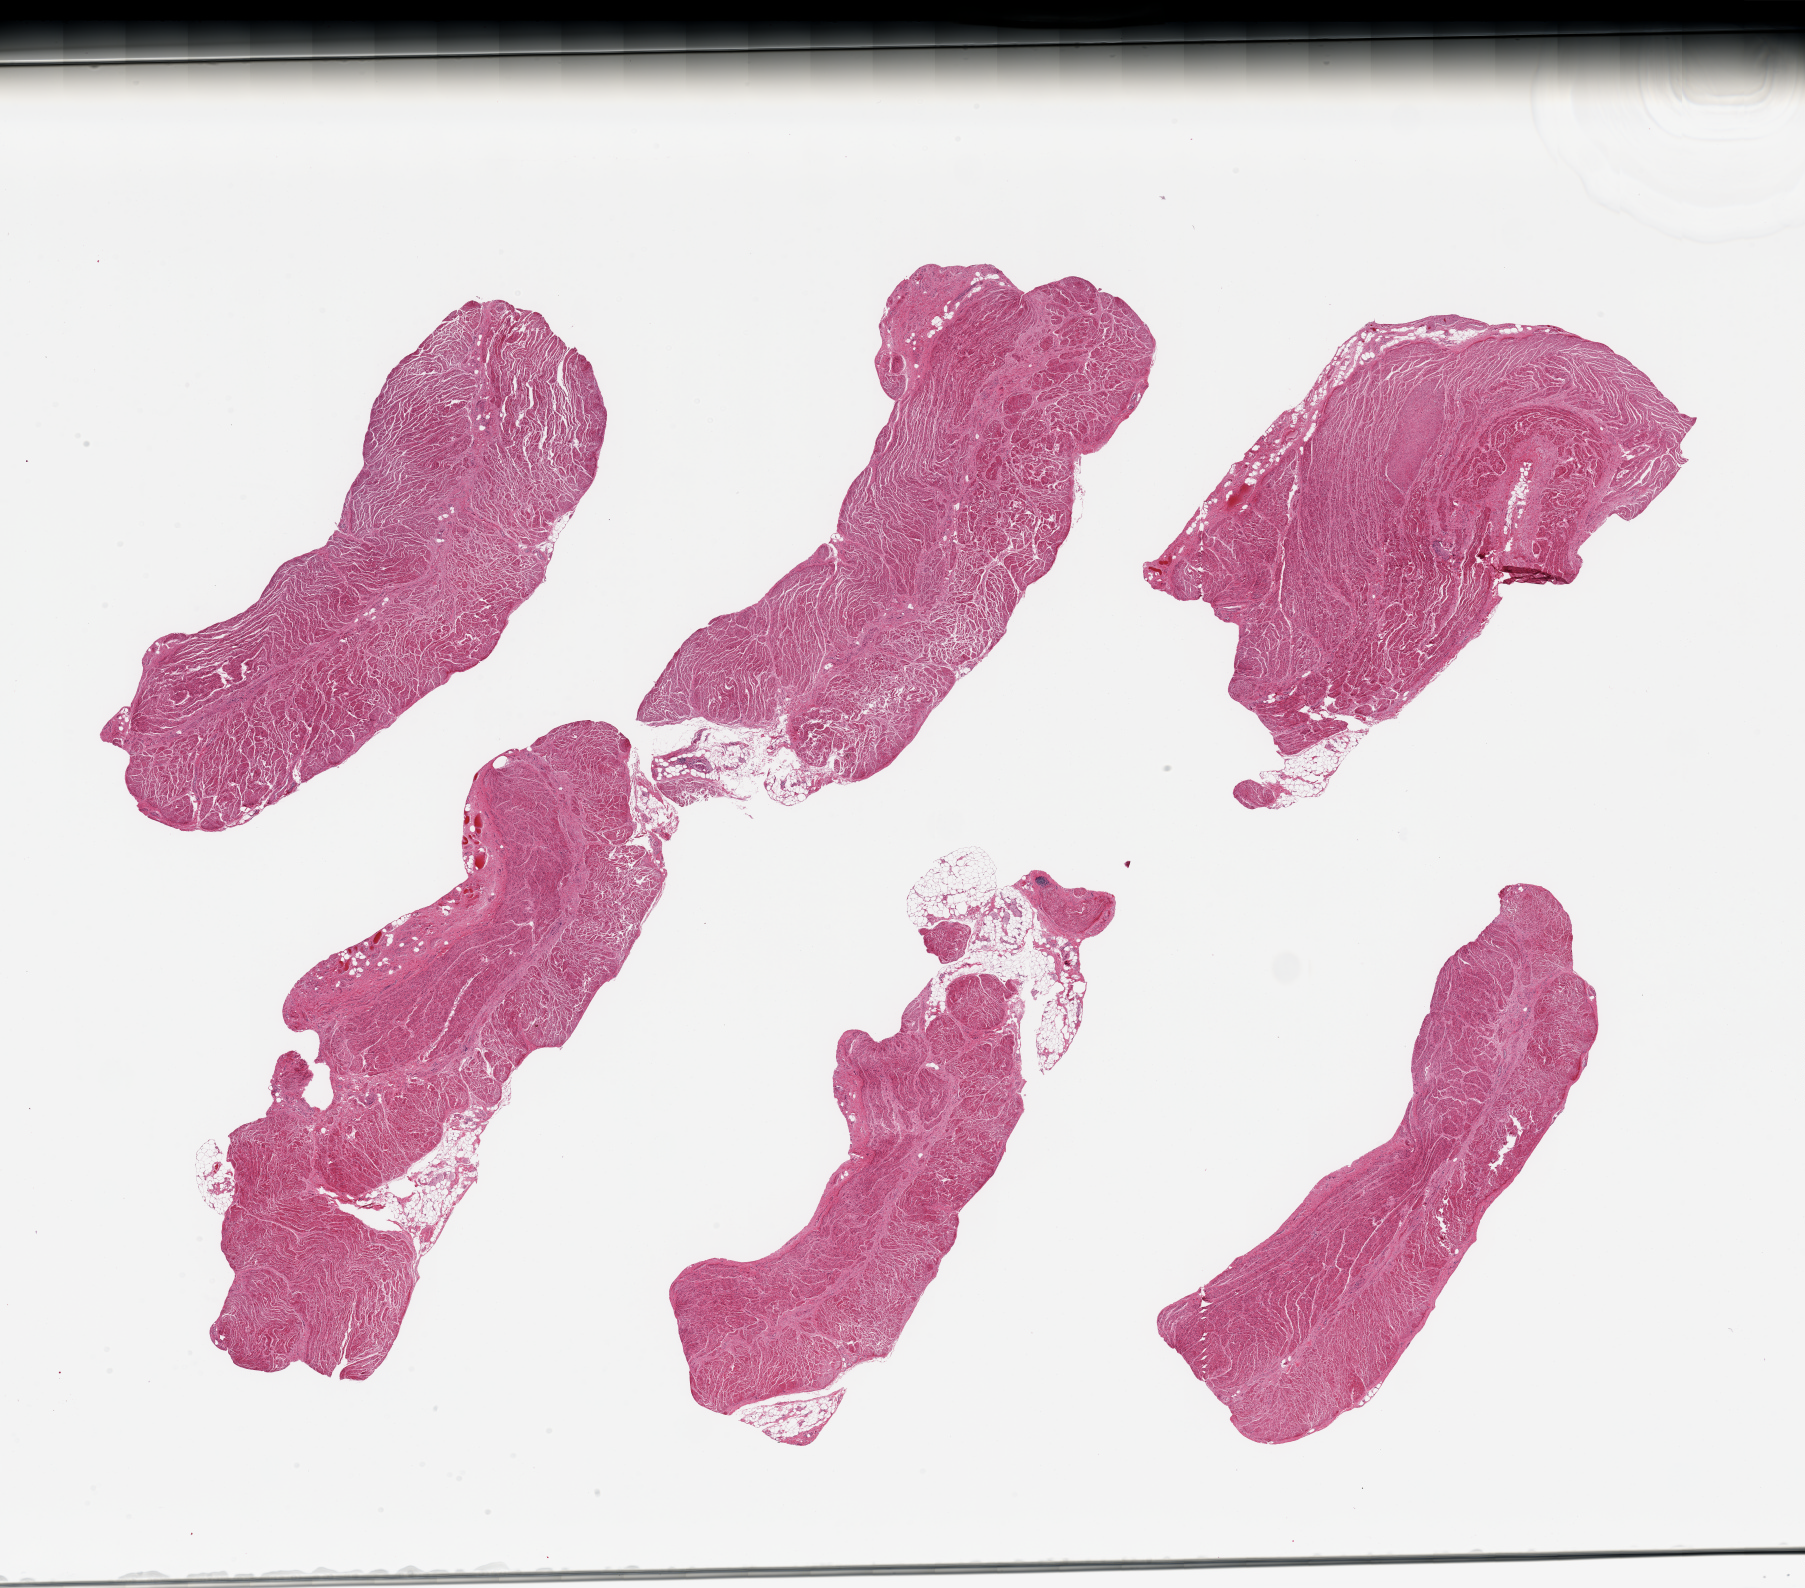
Digitized haematoxylin and eosin-stained section, shown as a low-resolution overview of the whole scanned area (about 28.5 x 25.1 mm, slide scanned at 20x). PAXgene-fixed paraffin-embedded (PFPE) section. Section of gastroesophageal junction (target tissue). Donor tissue sample.
Review note (as recorded): 6 pieces, confirmed target muscularis.